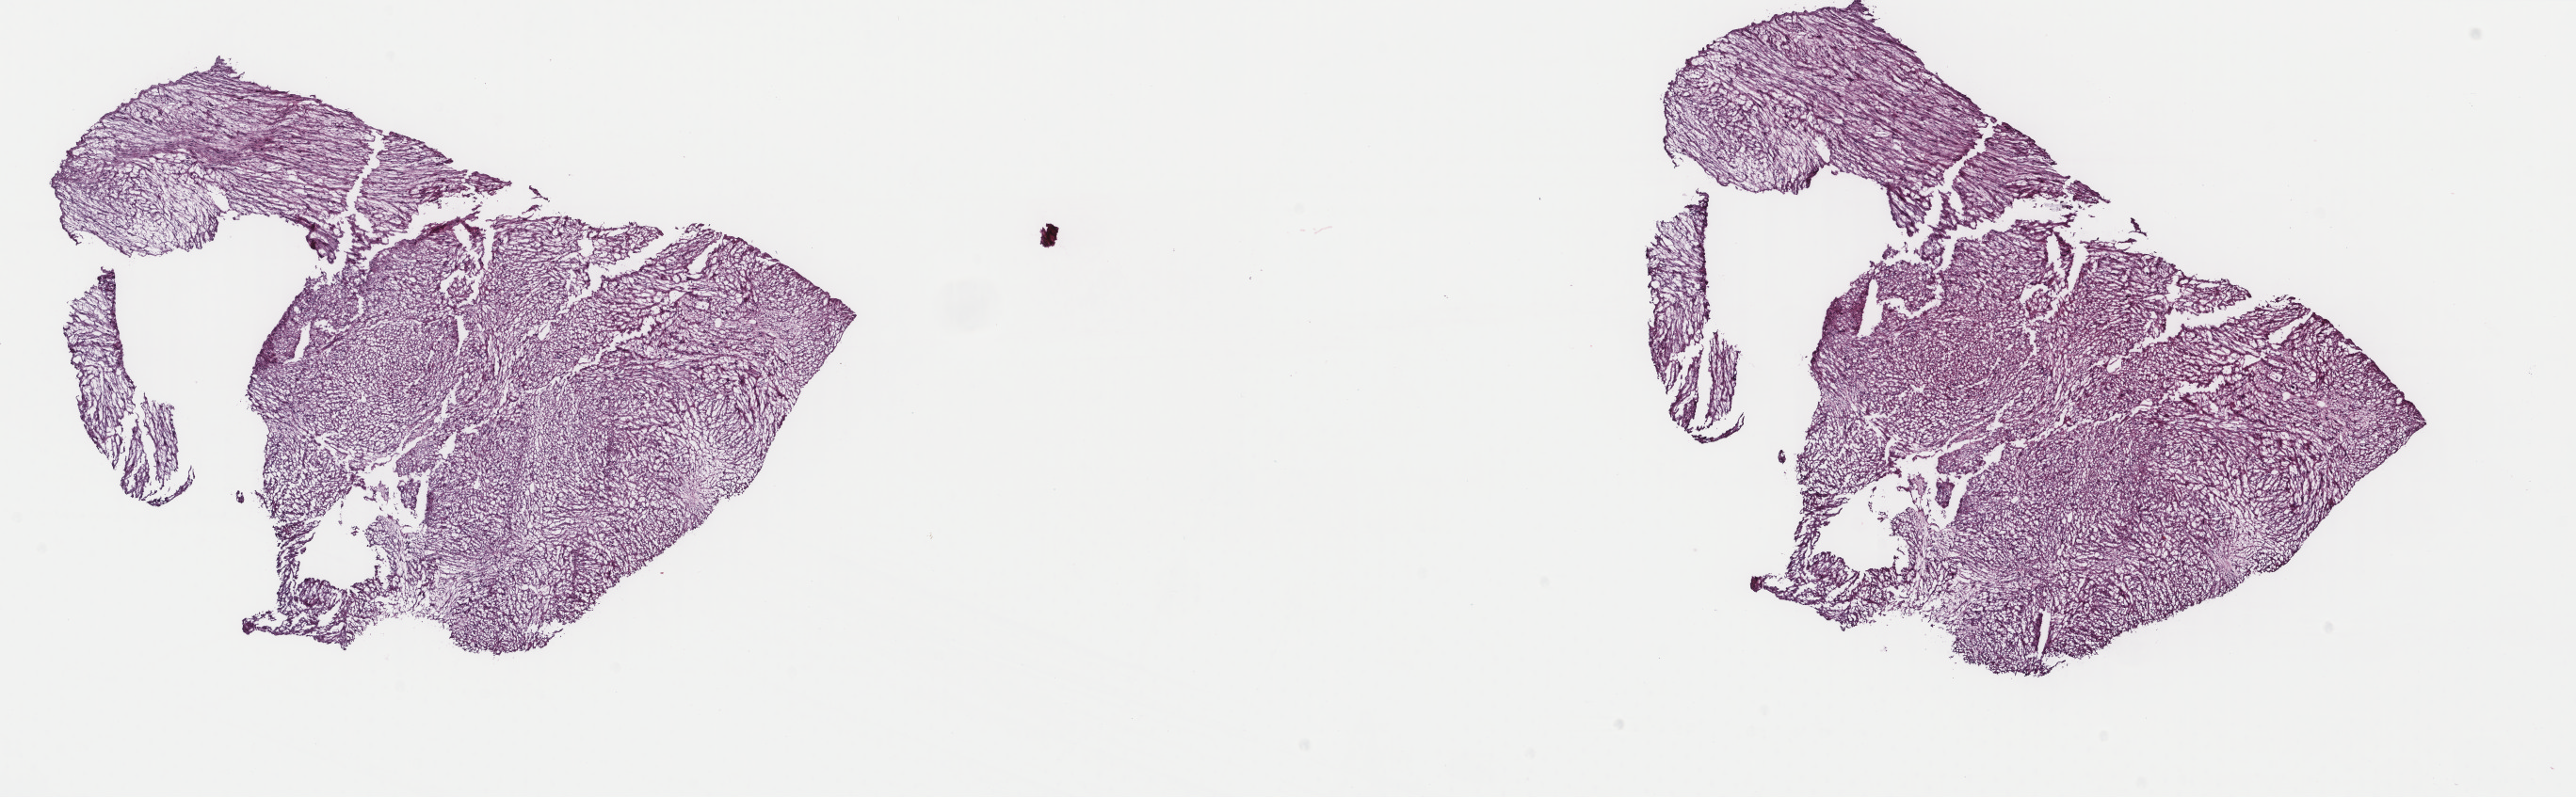
Digitized H&E-stained tissue section (whole slide) — whole scanned area (about 21.7 x 6.7 mm, slide scanned at 40x) shown as a low-resolution overview; frozen section; retroperitoneum and peritoneum, primary tumour sample. Male, age 41 years at initial diagnosis. Pathologist review of this section (percent, as recorded): tumour cells 85%, tumour nuclei 85%, normal cells 0%, stromal cells 15%, necrosis 0%. Infiltration values recorded for this section: lymphocyte infiltration 1%, monocyte infiltration 2%, neutrophil infiltration 1%.
Pathologic diagnosis: Leiomyosarcoma, NOS (retroperitoneum).